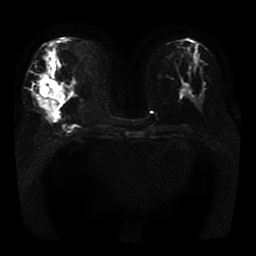
Breast MRI, one axial slice; slice 19 of 41 in the series (ordered by position); diffusion-weighted series; image 2 of 4 stored at this slice position (different b-values; order by instance number); 1.5 T; 5 mm slice thickness; 256 × 256 image matrix, field of view 330 × 330 mm. Female patient.
Outlined on this slice (manually delineated by an expert):
- tumour on diffusion-weighted imaging: box from (x=38, y=73) to (x=66, y=111) px